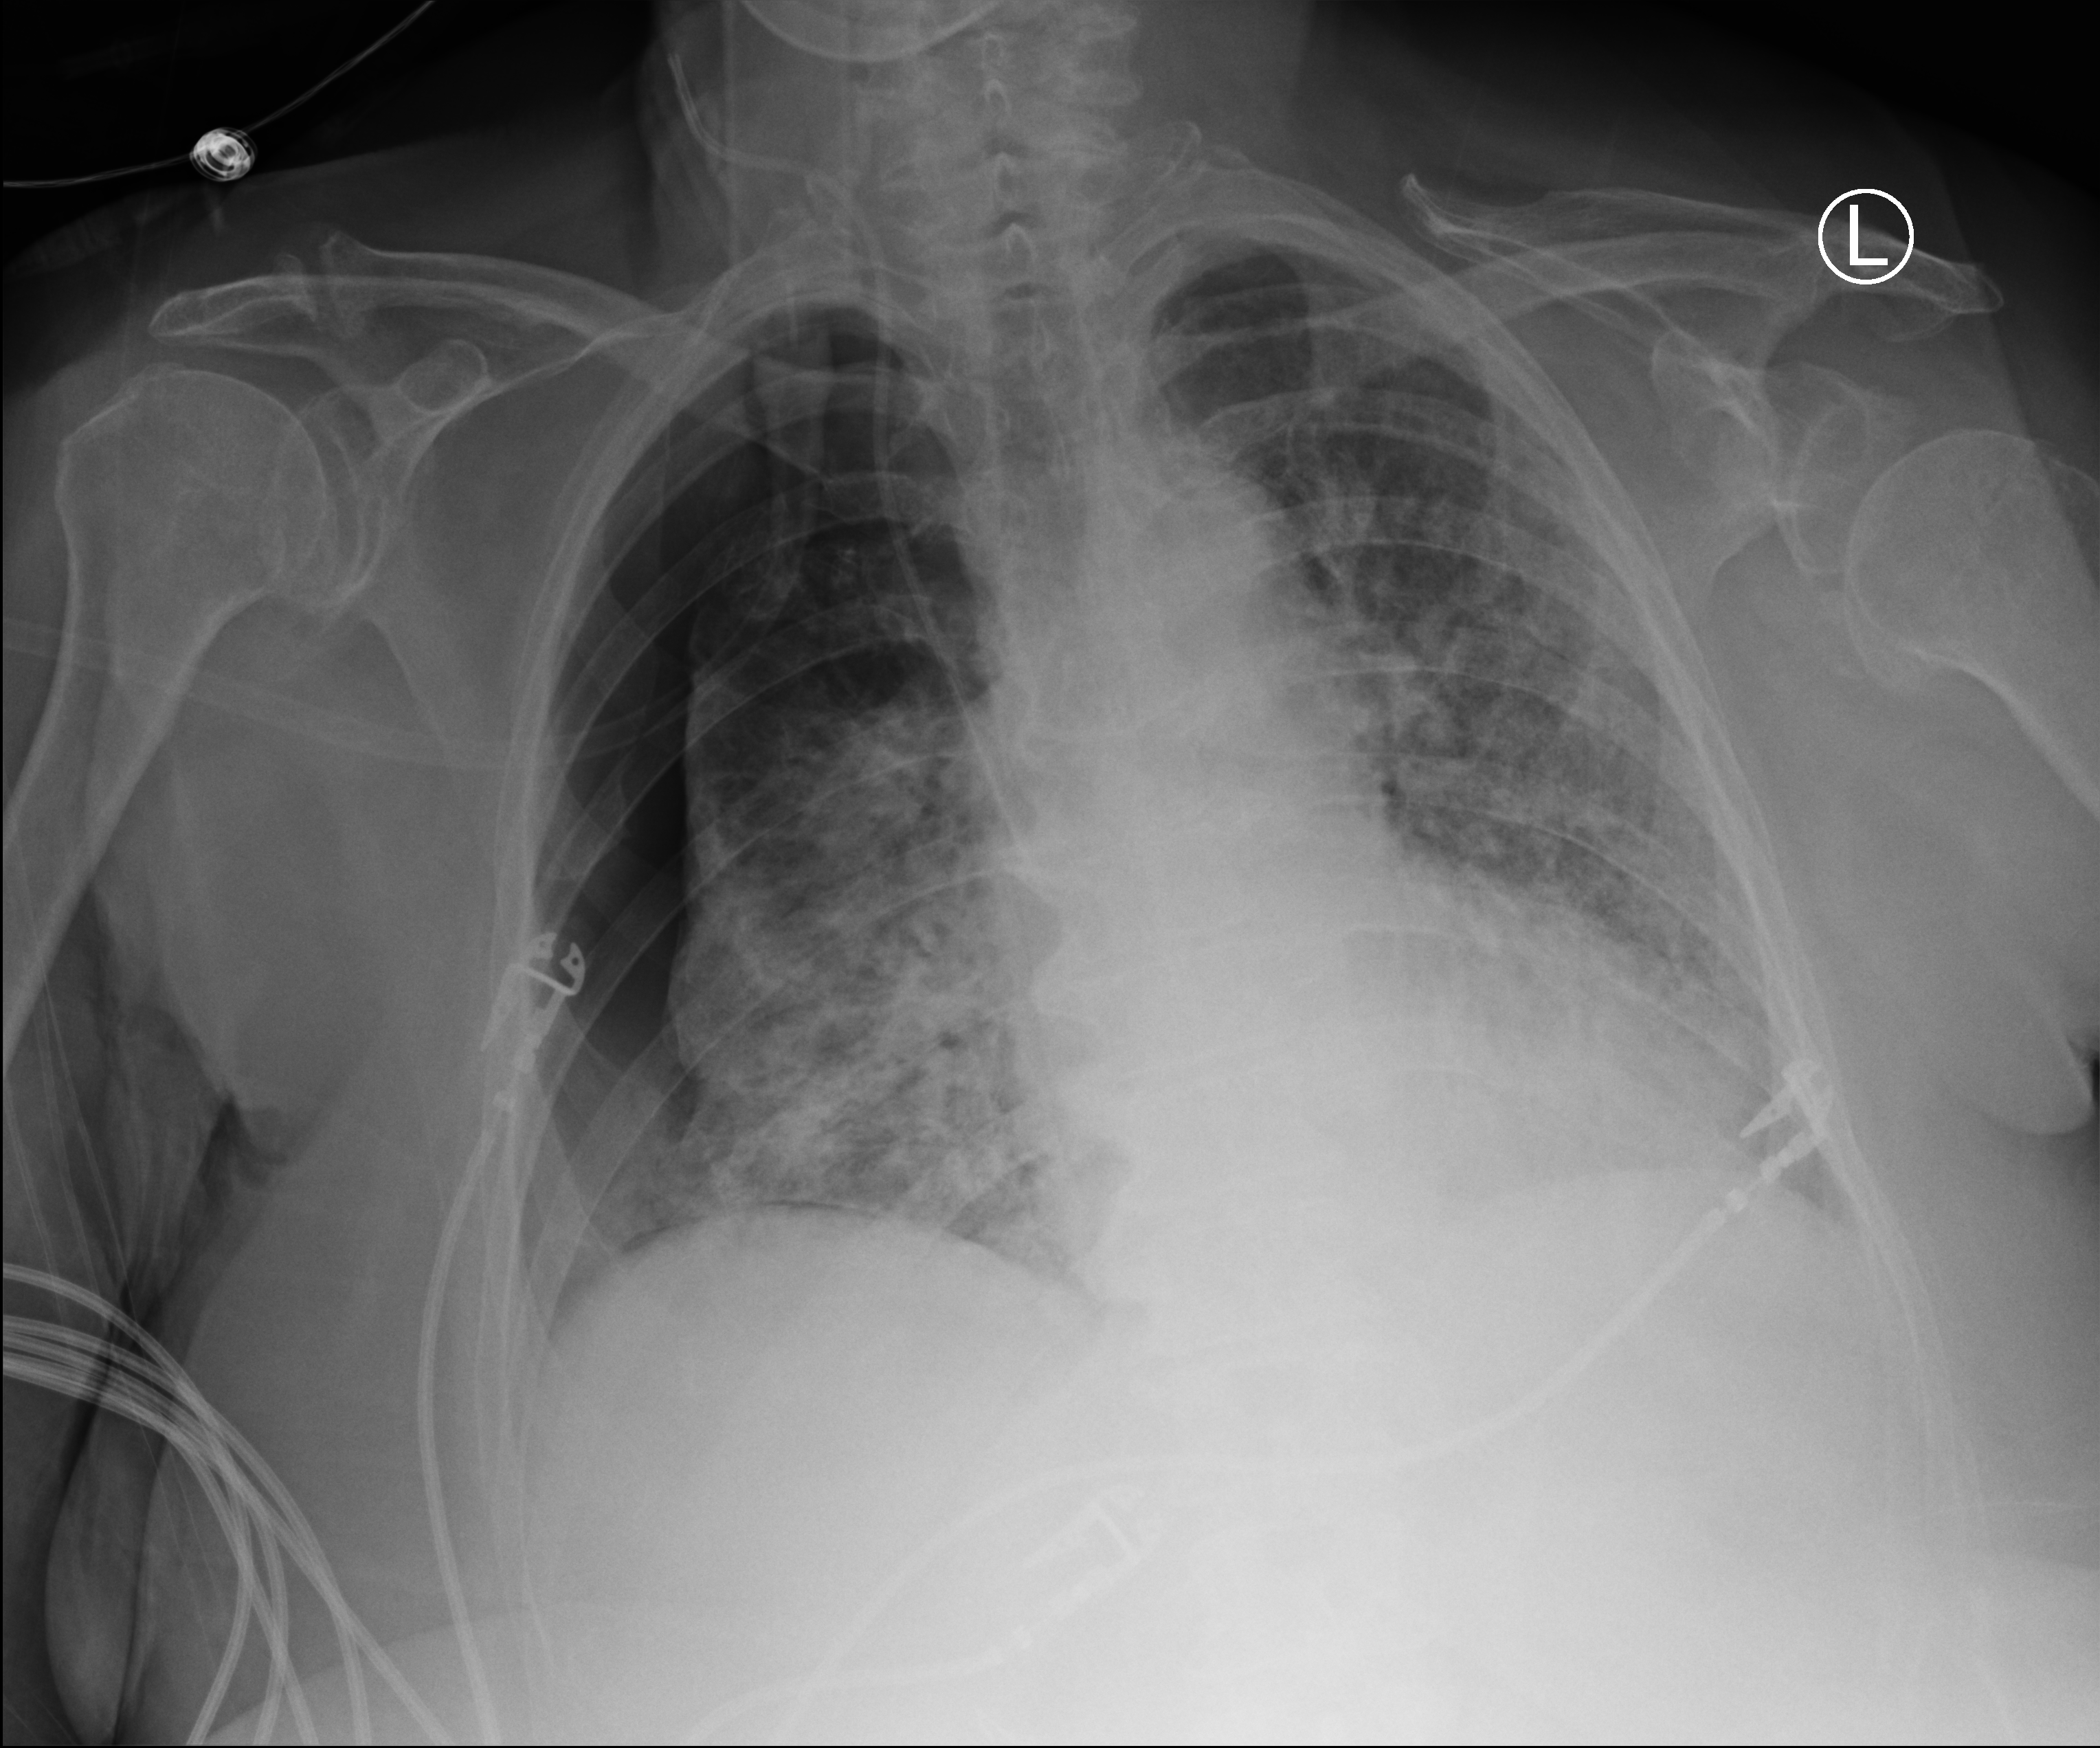
Portable chest radiograph. Patient hospitalised with COVID-19; female, aged 75–90 years.
Admission-level facts for this patient (not findings on this image; timing relative to this image not recorded): length of hospital stay: 56 days.